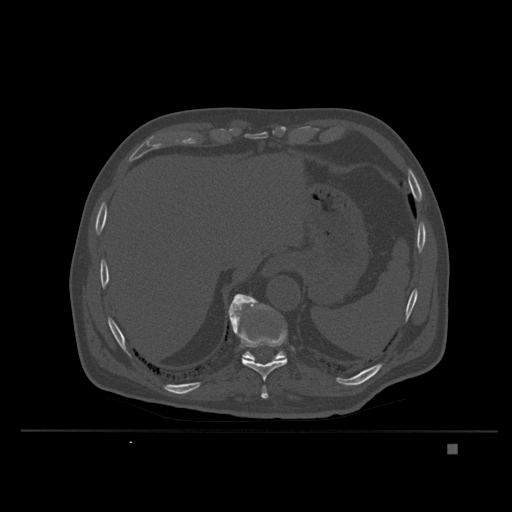
CT including the spine, one axial slice. Slice 191 of 435 in the series (ordered by position). Bone window (W 1800 / L 400 HU). 1.5 mm slice thickness. 512 × 512 image matrix. Male patient, age 73 years. From the clinical record (not read from this slice): primary cancer: skin.
Outlined on this slice (semi-automatic segmentation, software-assisted and operator-edited):
- T10 vertebra: bounding box <231,316,288,381> (left, top, right, bottom; pixels)
- T11 vertebra: <228,294,288,362>
- T9 vertebra: <261,385,269,400>